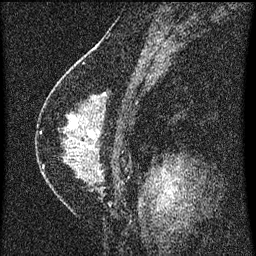
Breast MRI (dynamic contrast-enhanced), one sagittal slice. Dynamic contrast-enhanced series, image 2 of 3 at this slice position (ordered by acquisition). 1.5 T. TE 4.2 ms, TR 8 ms. 256 × 256 image matrix, field of view 180 × 180 mm. Female patient, age 47 years.
Outlined on this slice (semi-automatically segmented with operator editing):
- analysis volume of interest (the breast-tissue region the enhancement analysis was run in; not a lesion): bounding box (x1, y1, x2, y2) in pixels: (42, 92, 130, 199)
- tumour enhancement mask (voxels above the 70 % enhancement threshold inside the analysis volume of interest): (70, 94, 105, 135)